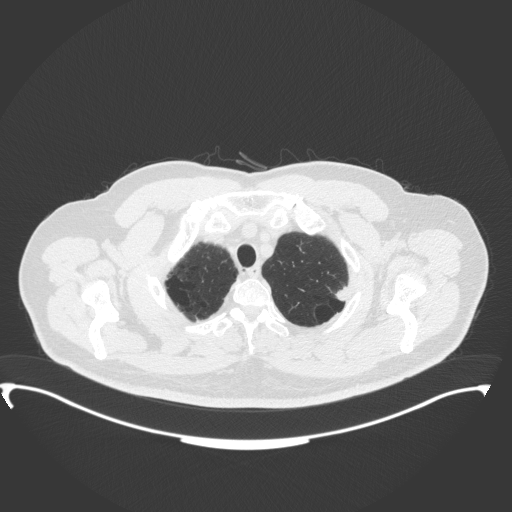
Chest CT, one axial slice. Position 327 of 350 along the scan axis. Reconstruction kernel B31f. 120 kVp. Lung window (W 1500 / L -600 HU). 1 mm slice thickness. 512 × 512 image matrix, field of view 459 × 459 mm. Male patient, age 64 years. From the clinical record (not read from this slice): clinical TNM (as recorded): T1c N1 M1.
Structures marked on this image (rectangle marked by the reading radiologist):
- lung tumour (recorded histology: adenocarcinoma): bounding box <330,282,351,303> (left, top, right, bottom; pixels)